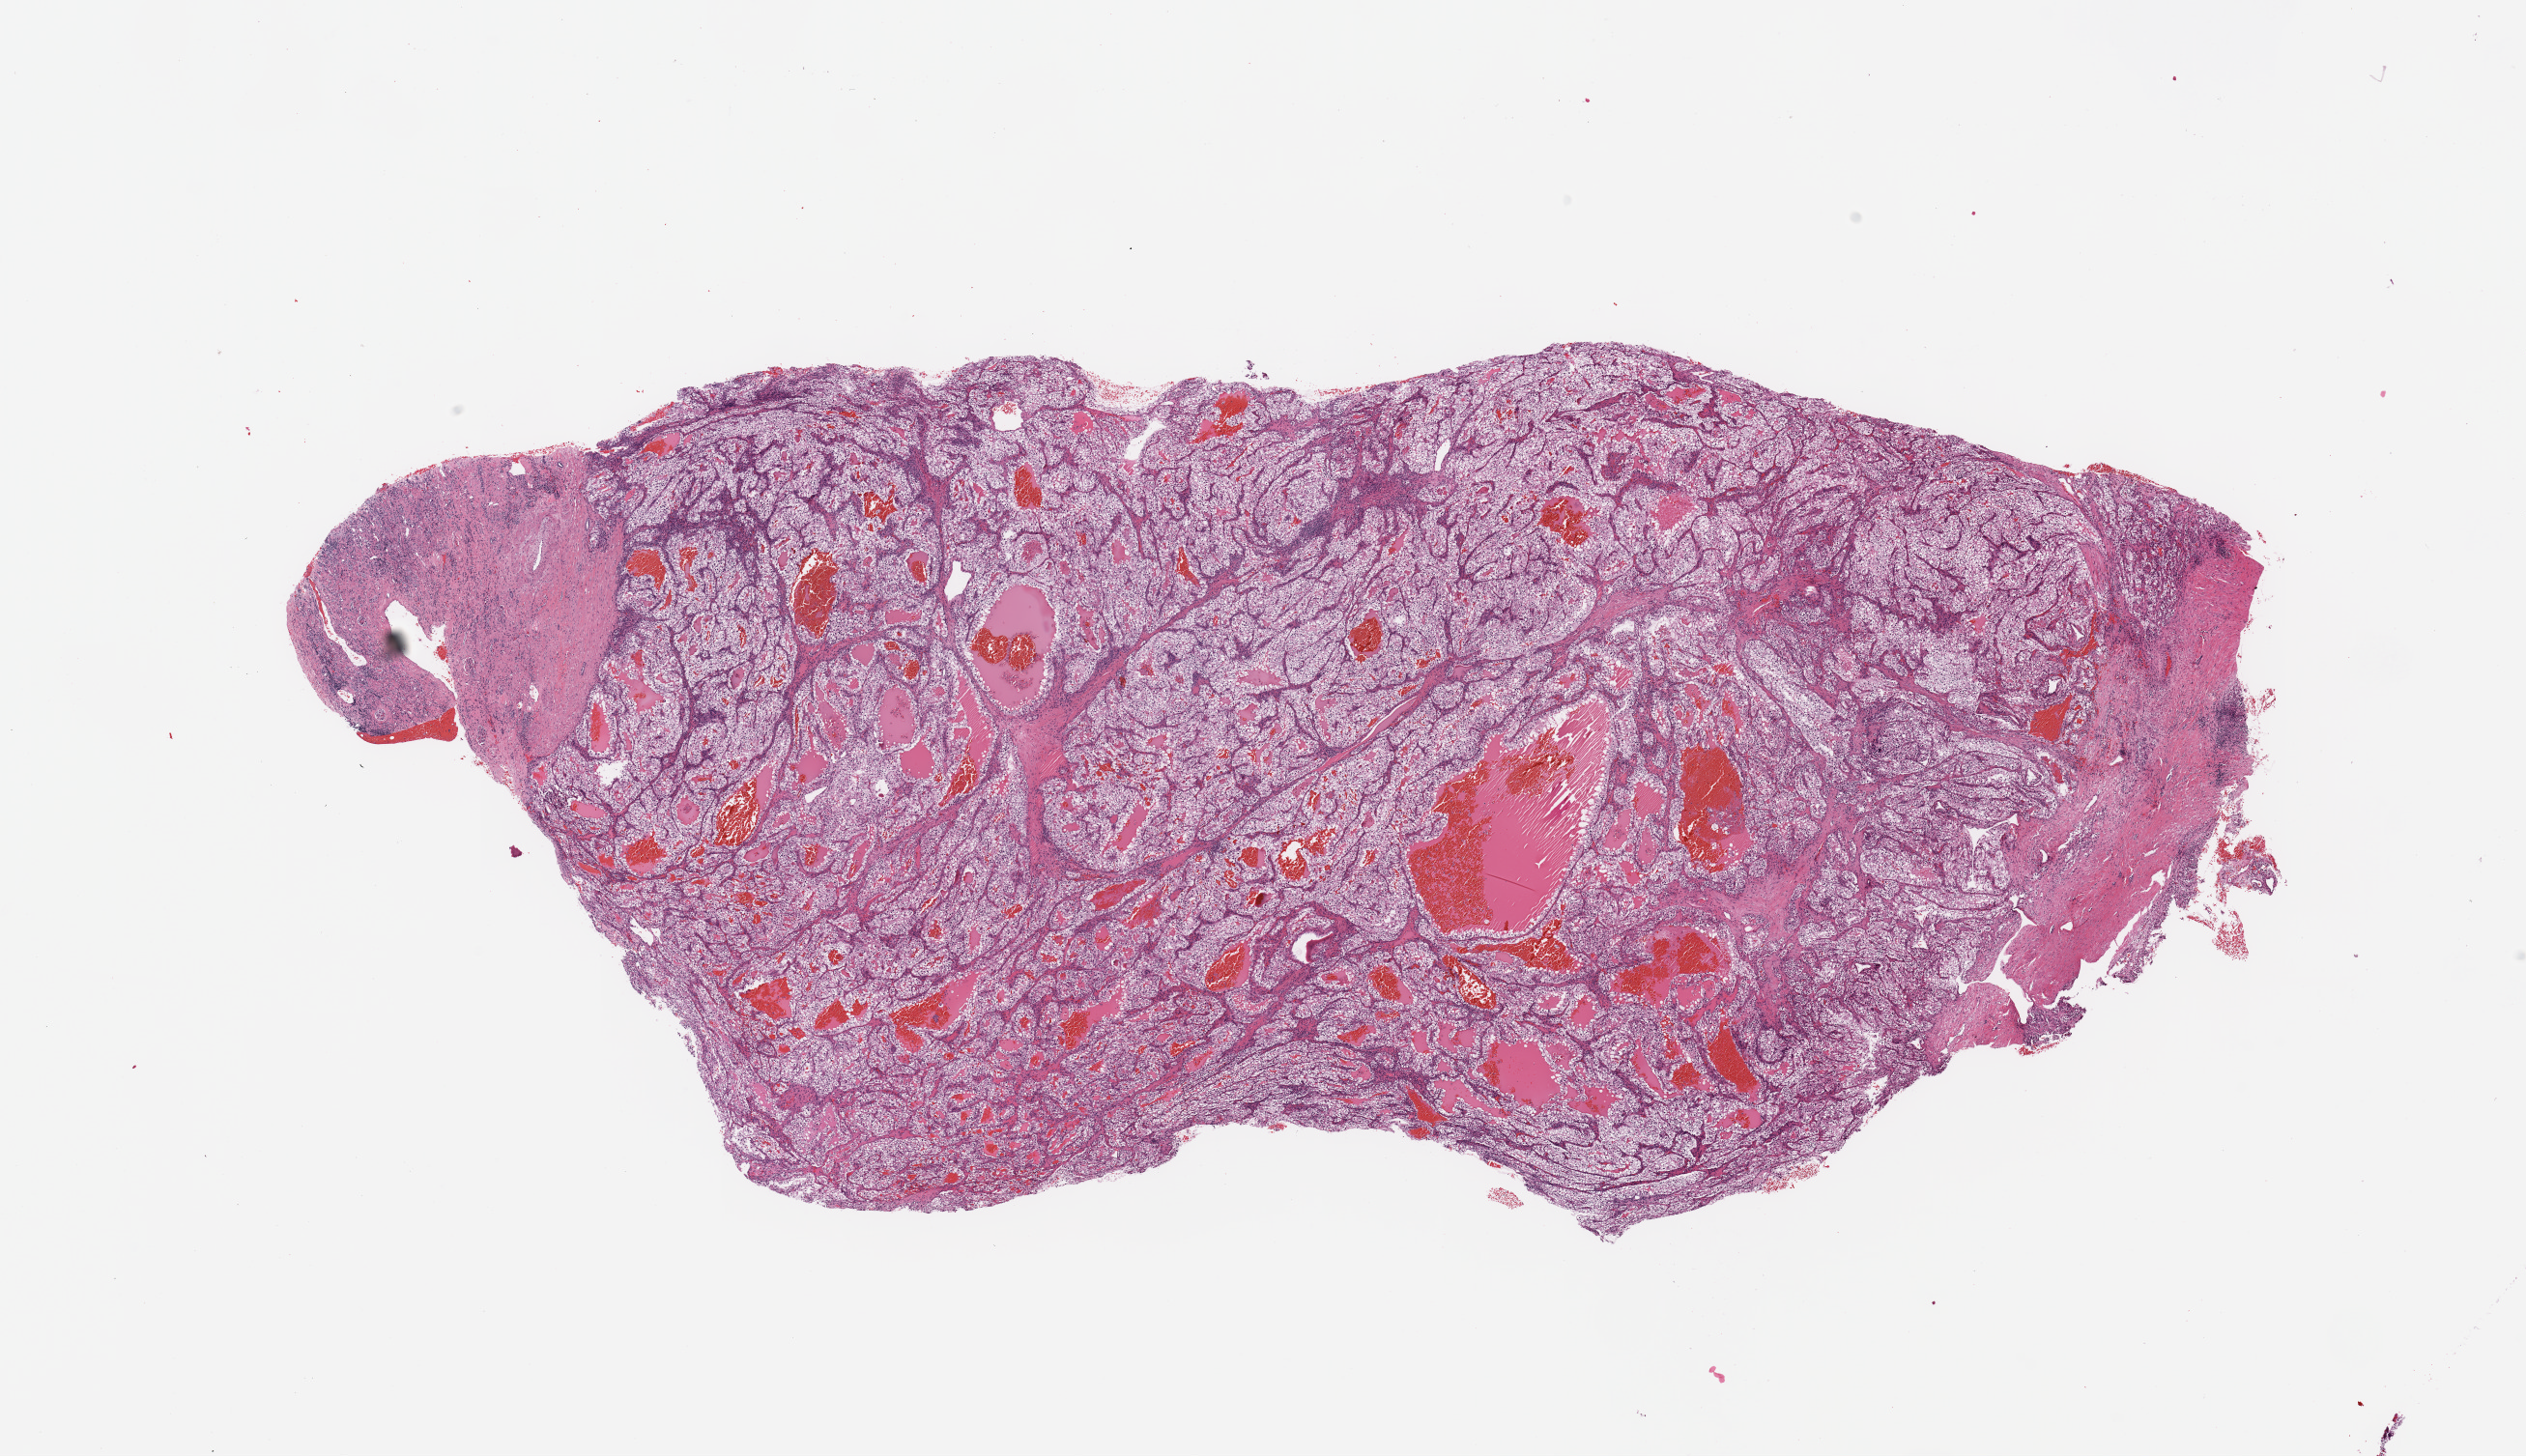
H&E whole-slide image — shown as a low-resolution overview of the whole scanned area (about 20.7 x 11.9 mm, from a 20x scan). Kidney, tumour tissue. 55-year-old male patient.
Diagnosis: Renal cell carcinoma, NOS.